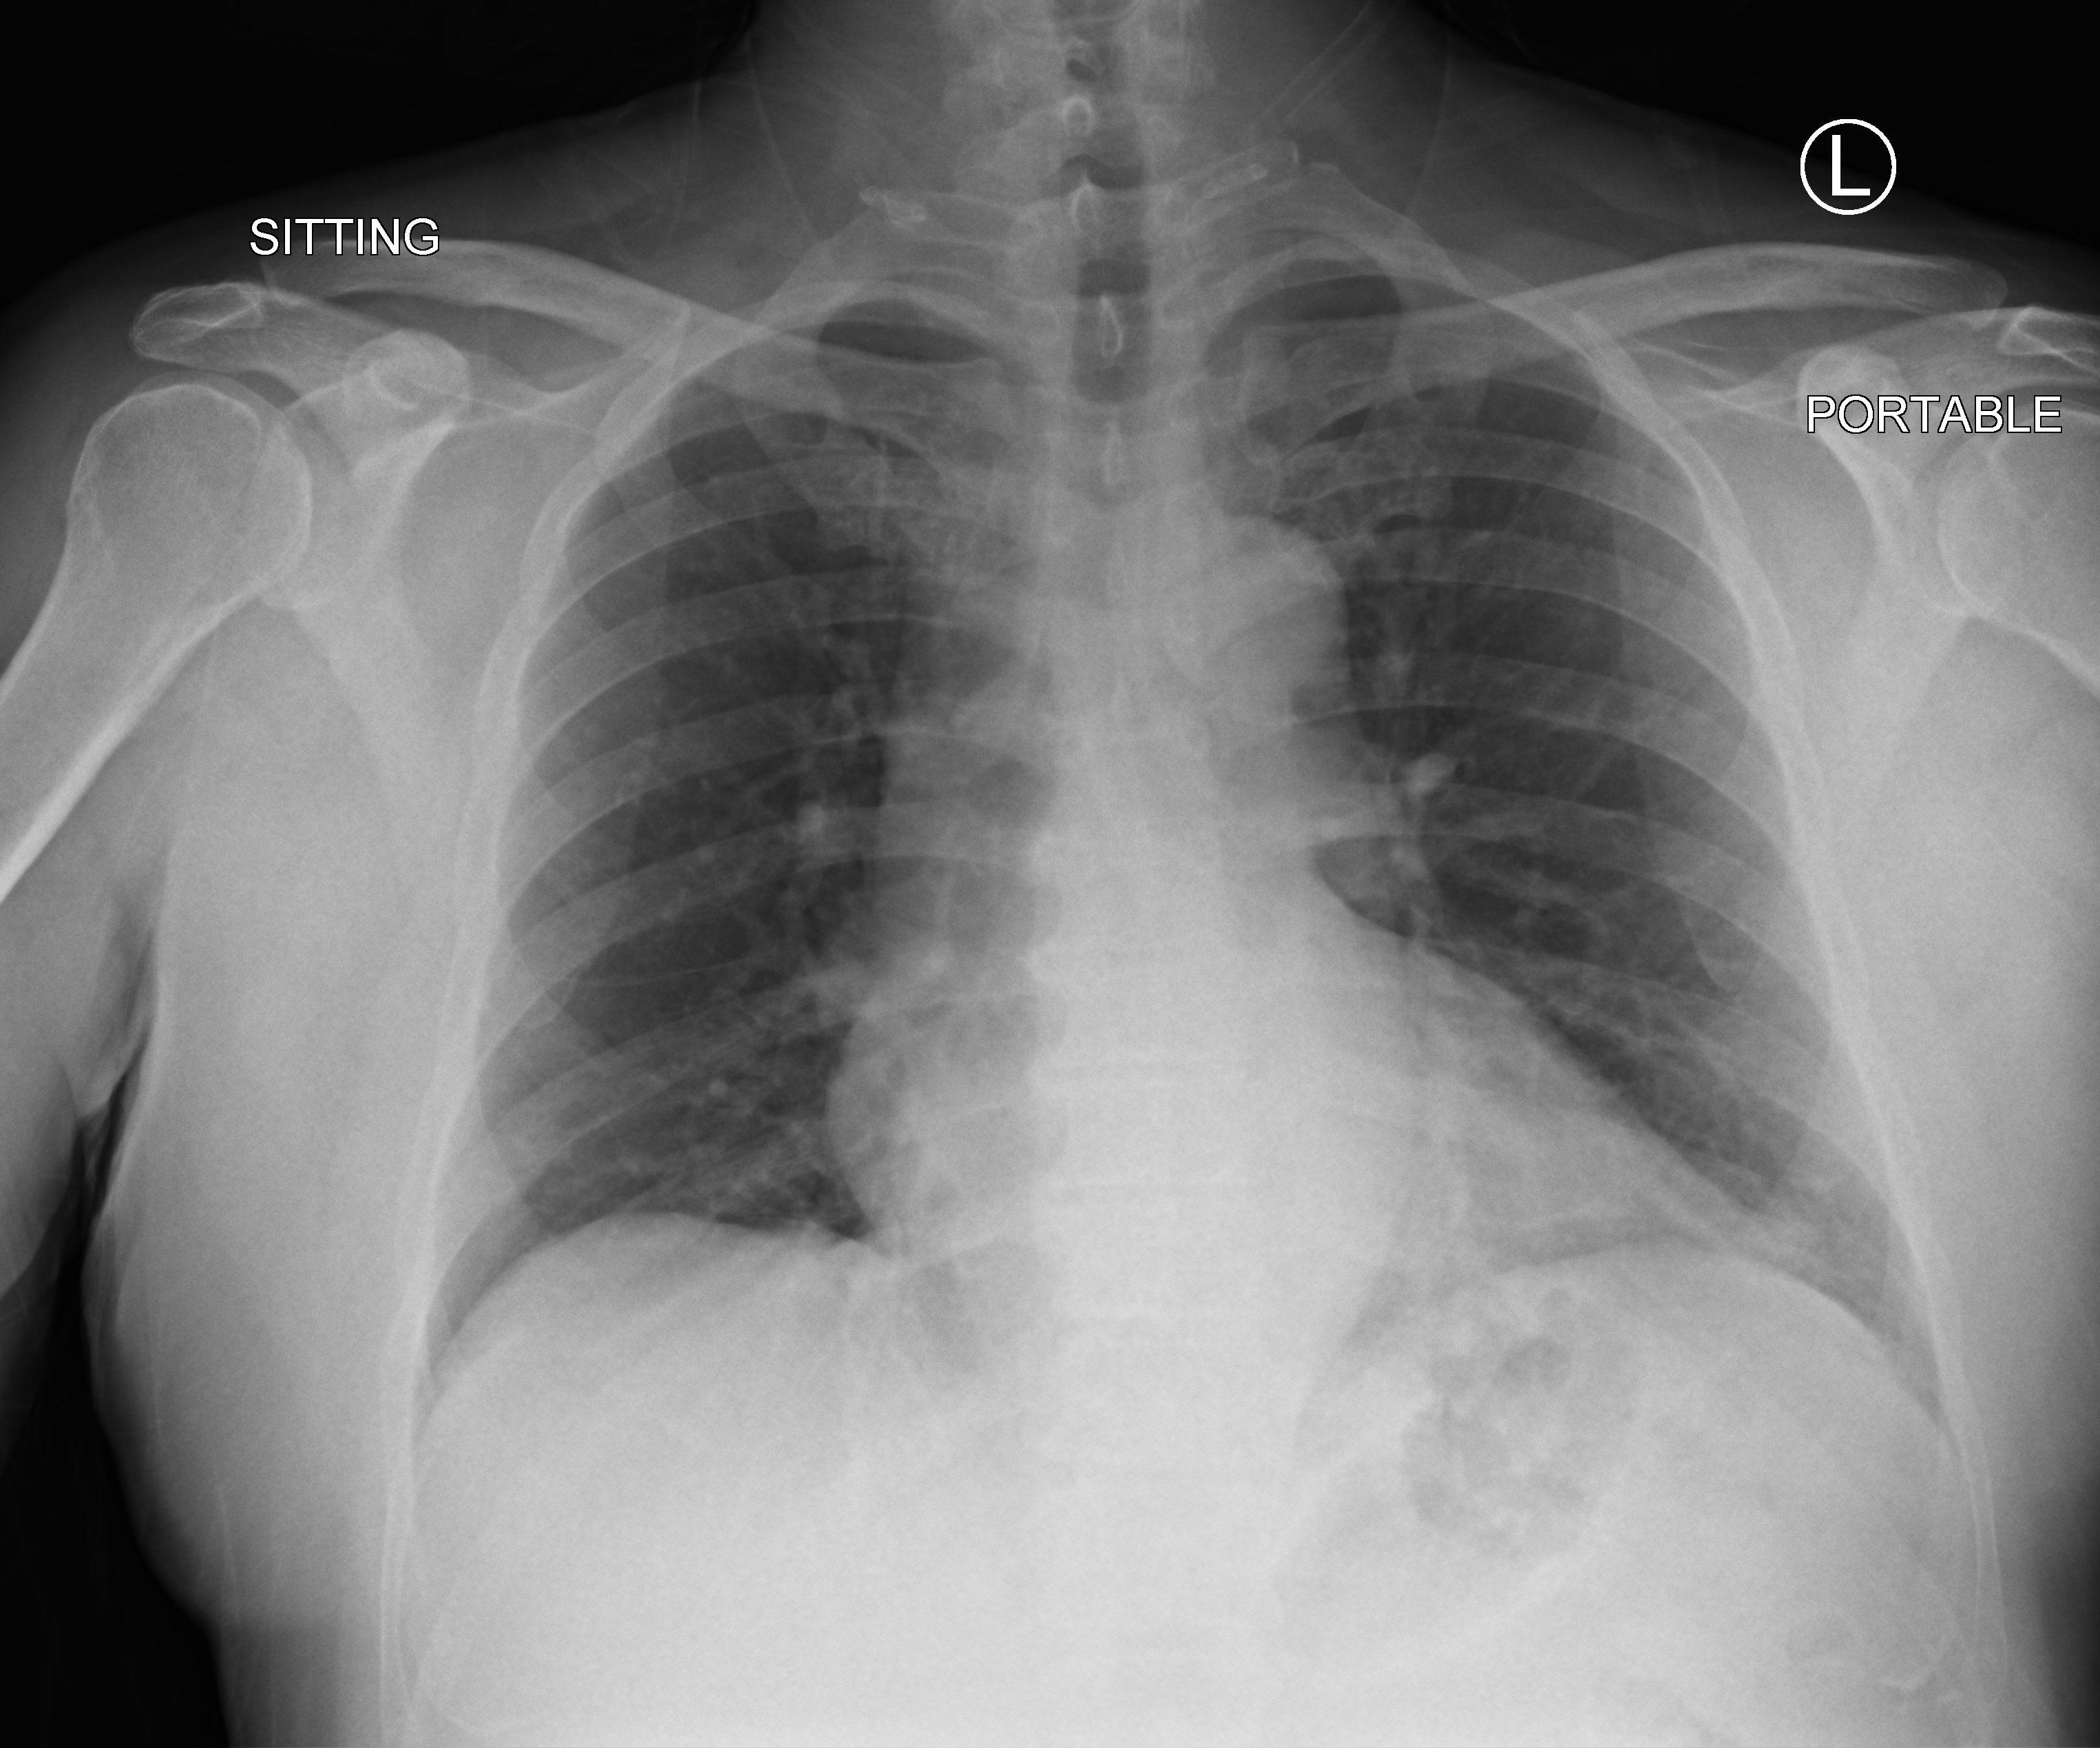
Portable chest radiograph; anteroposterior (AP) projection. Male patient hospitalised with COVID-19, age 18–59 years.
From the hospital-stay record, not from the radiograph (when in the stay this image was taken is not recorded): smoking status (admission record): never; mechanically ventilated during this hospital stay: no; hypertension (admission record): no.